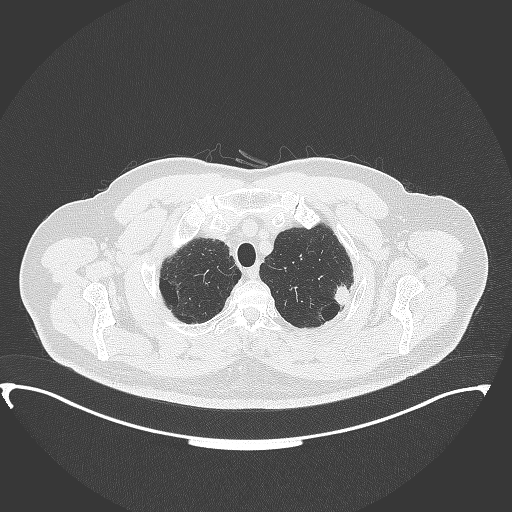
Chest CT, one axial slice; slice 321 of 350 in the series (ordered by position); reconstruction kernel B70f; lung window (W 1500 / L -600 HU); 1 mm slice thickness; 512 × 512 image matrix, field of view 459 × 459 mm. Male patient, age 64 years. Case-level facts recorded for this patient, not image findings: clinical TNM (as recorded): T1c N1 M1.
Outlined on this slice (bounding box drawn by a radiologist):
- lung tumour (recorded histology: adenocarcinoma): box from (x=328, y=282) to (x=357, y=307) px